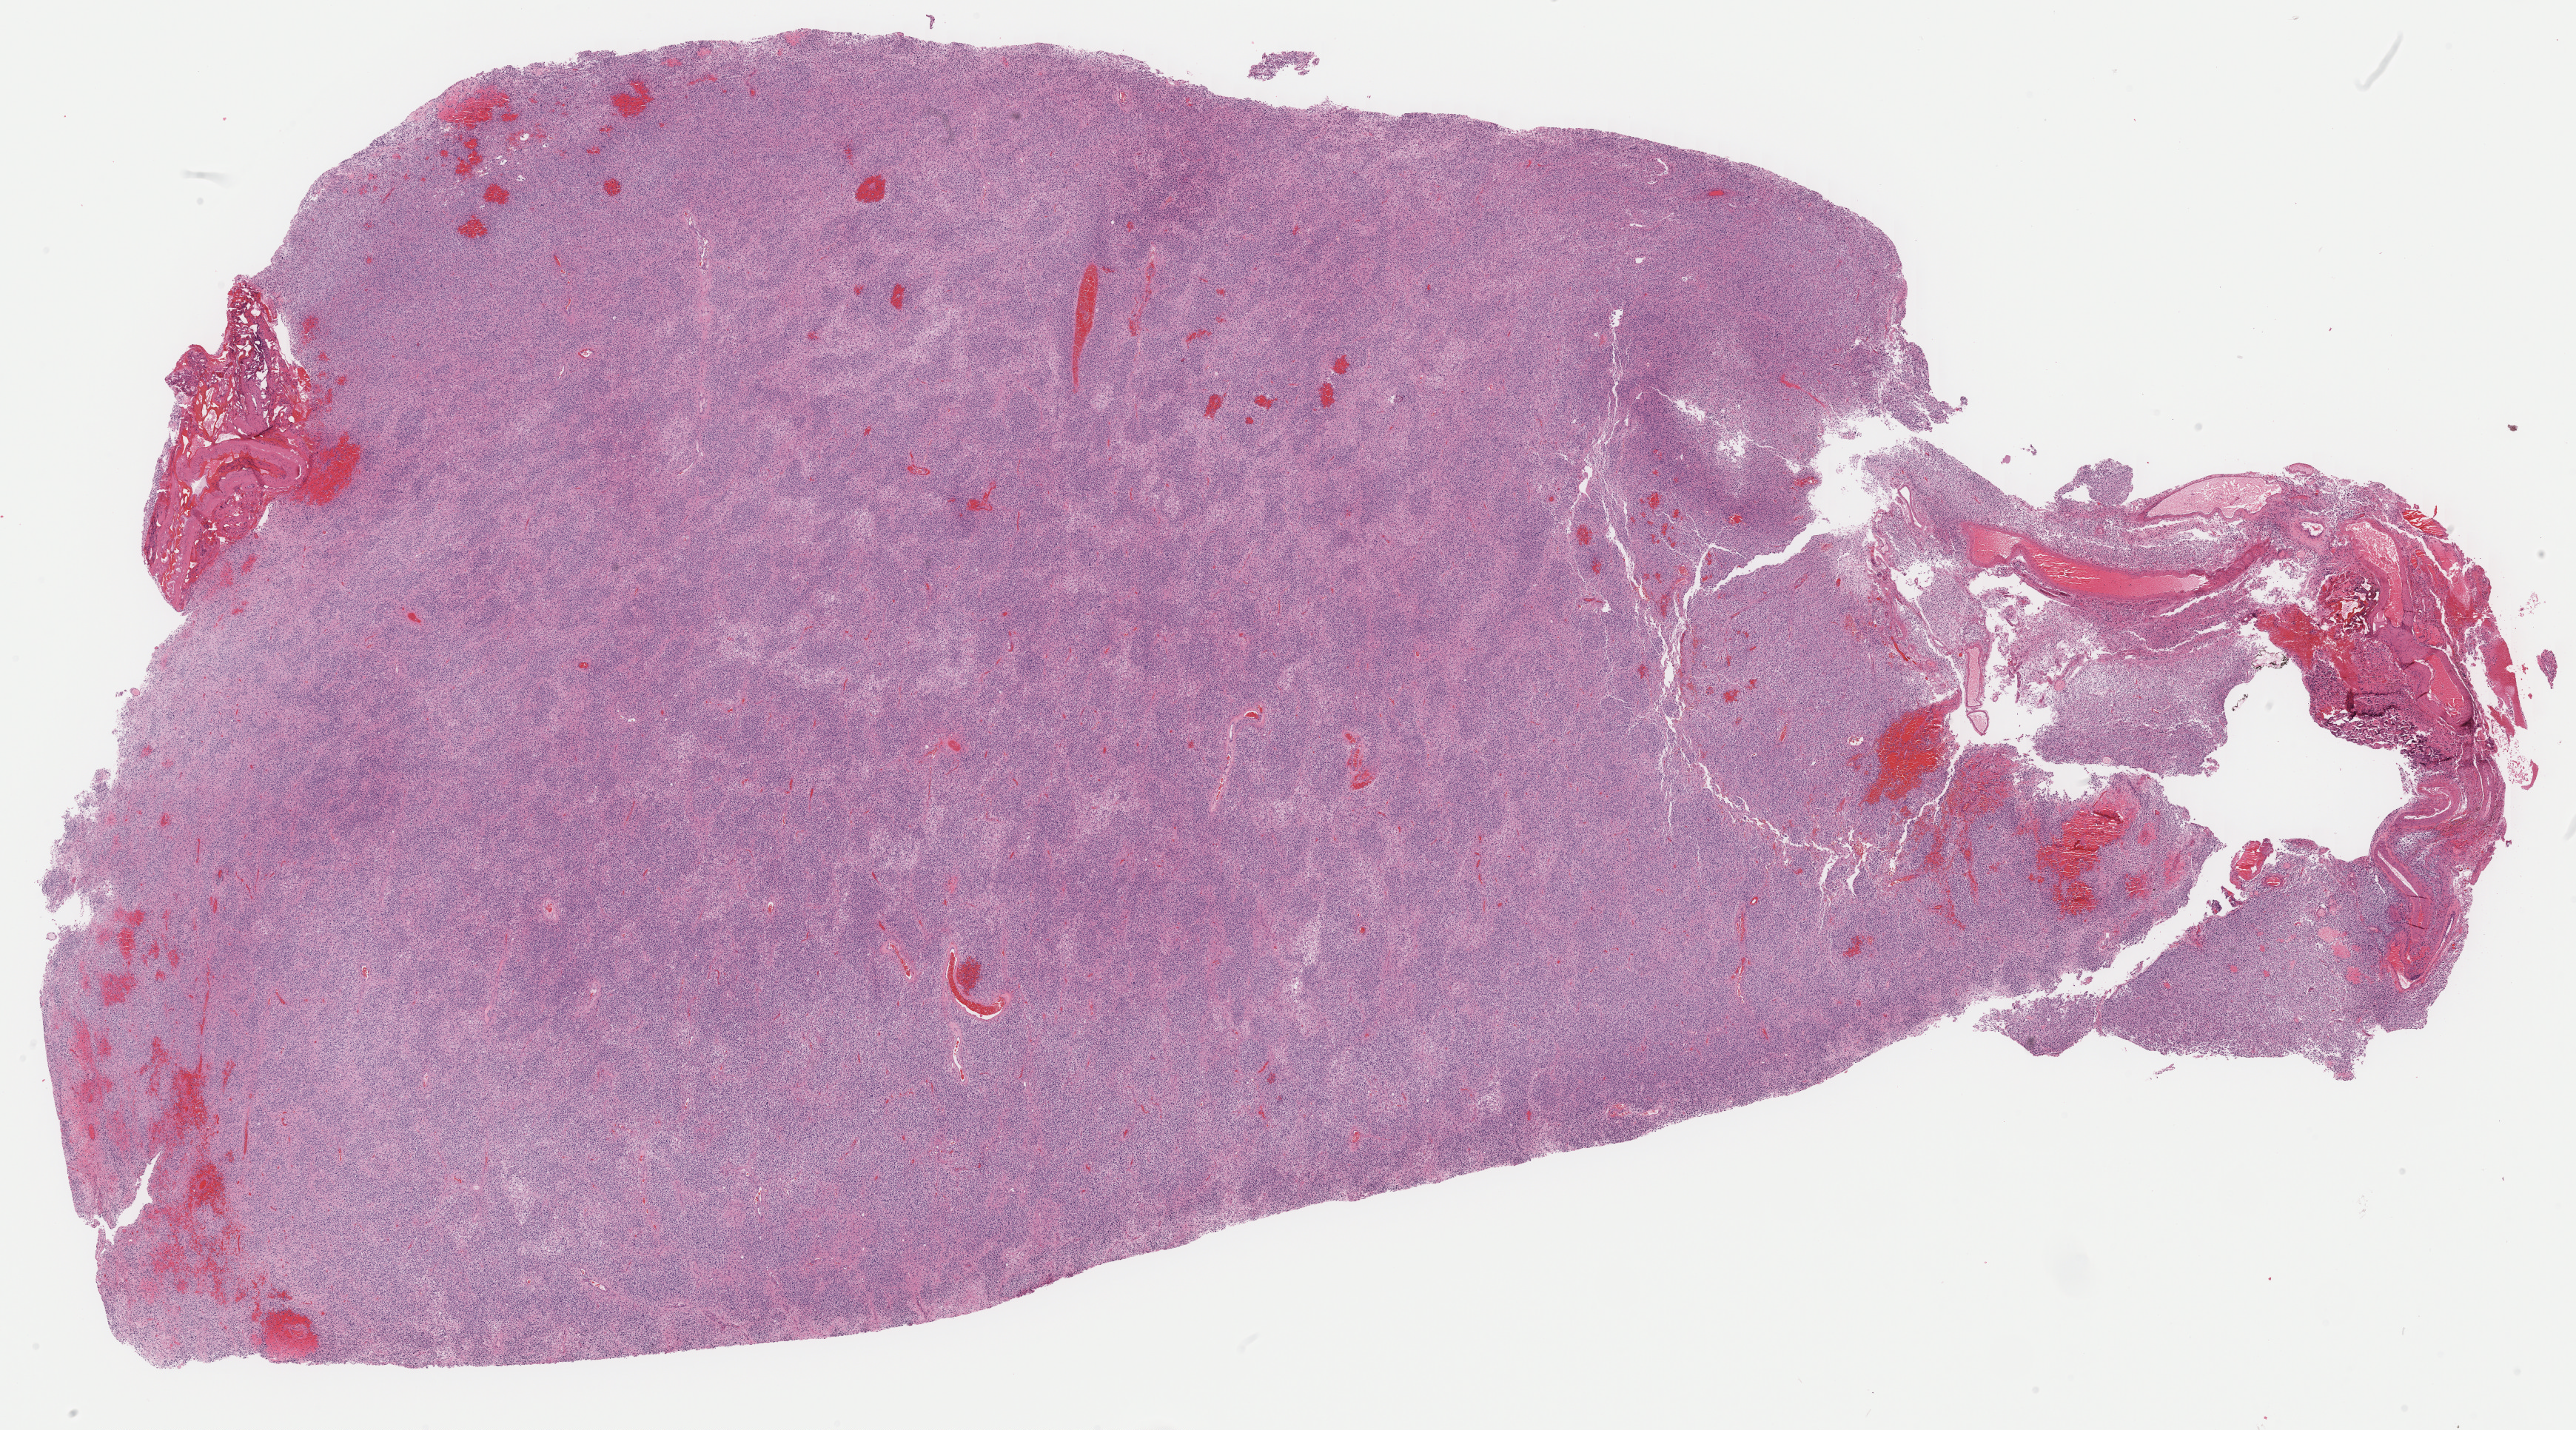
Whole-slide histology image, H&E-stained, whole scanned area (about 27.4 x 15.2 mm) shown as a low-resolution overview; FFPE section; primary tumour sample from the brain. Patient: male, age at initial diagnosis 36 years. Histologic grade: G3 (poorly differentiated).
* pathologic diagnosis: Mixed glioma (cerebrum)